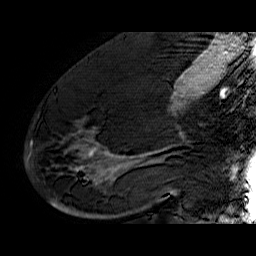
Breast MRI (dynamic contrast-enhanced), one sagittal slice; position 32 of 60 along the scan axis; dynamic contrast-enhanced series, time point 2 of 6 at this slice position (early post-contrast); 1.5 T; TE 6.4 ms, TR 32.9 ms; 4 mm slice thickness; 256 × 256 image matrix. Female patient. Case-level facts recorded for this patient, not image findings: setting: breast cancer imaged before/during neoadjuvant chemotherapy; receptor status: HR-positive, HER2-negative.
Annotated regions visible in this slice (semi-automatically segmented with operator editing):
- analysis volume of interest (the breast-tissue region the enhancement analysis was run in; not a lesion): box from (x=38, y=74) to (x=176, y=210) px
- tumour enhancement mask (voxels above the 100 % enhancement threshold inside the analysis volume of interest): (x=76, y=114)–(x=176, y=195)